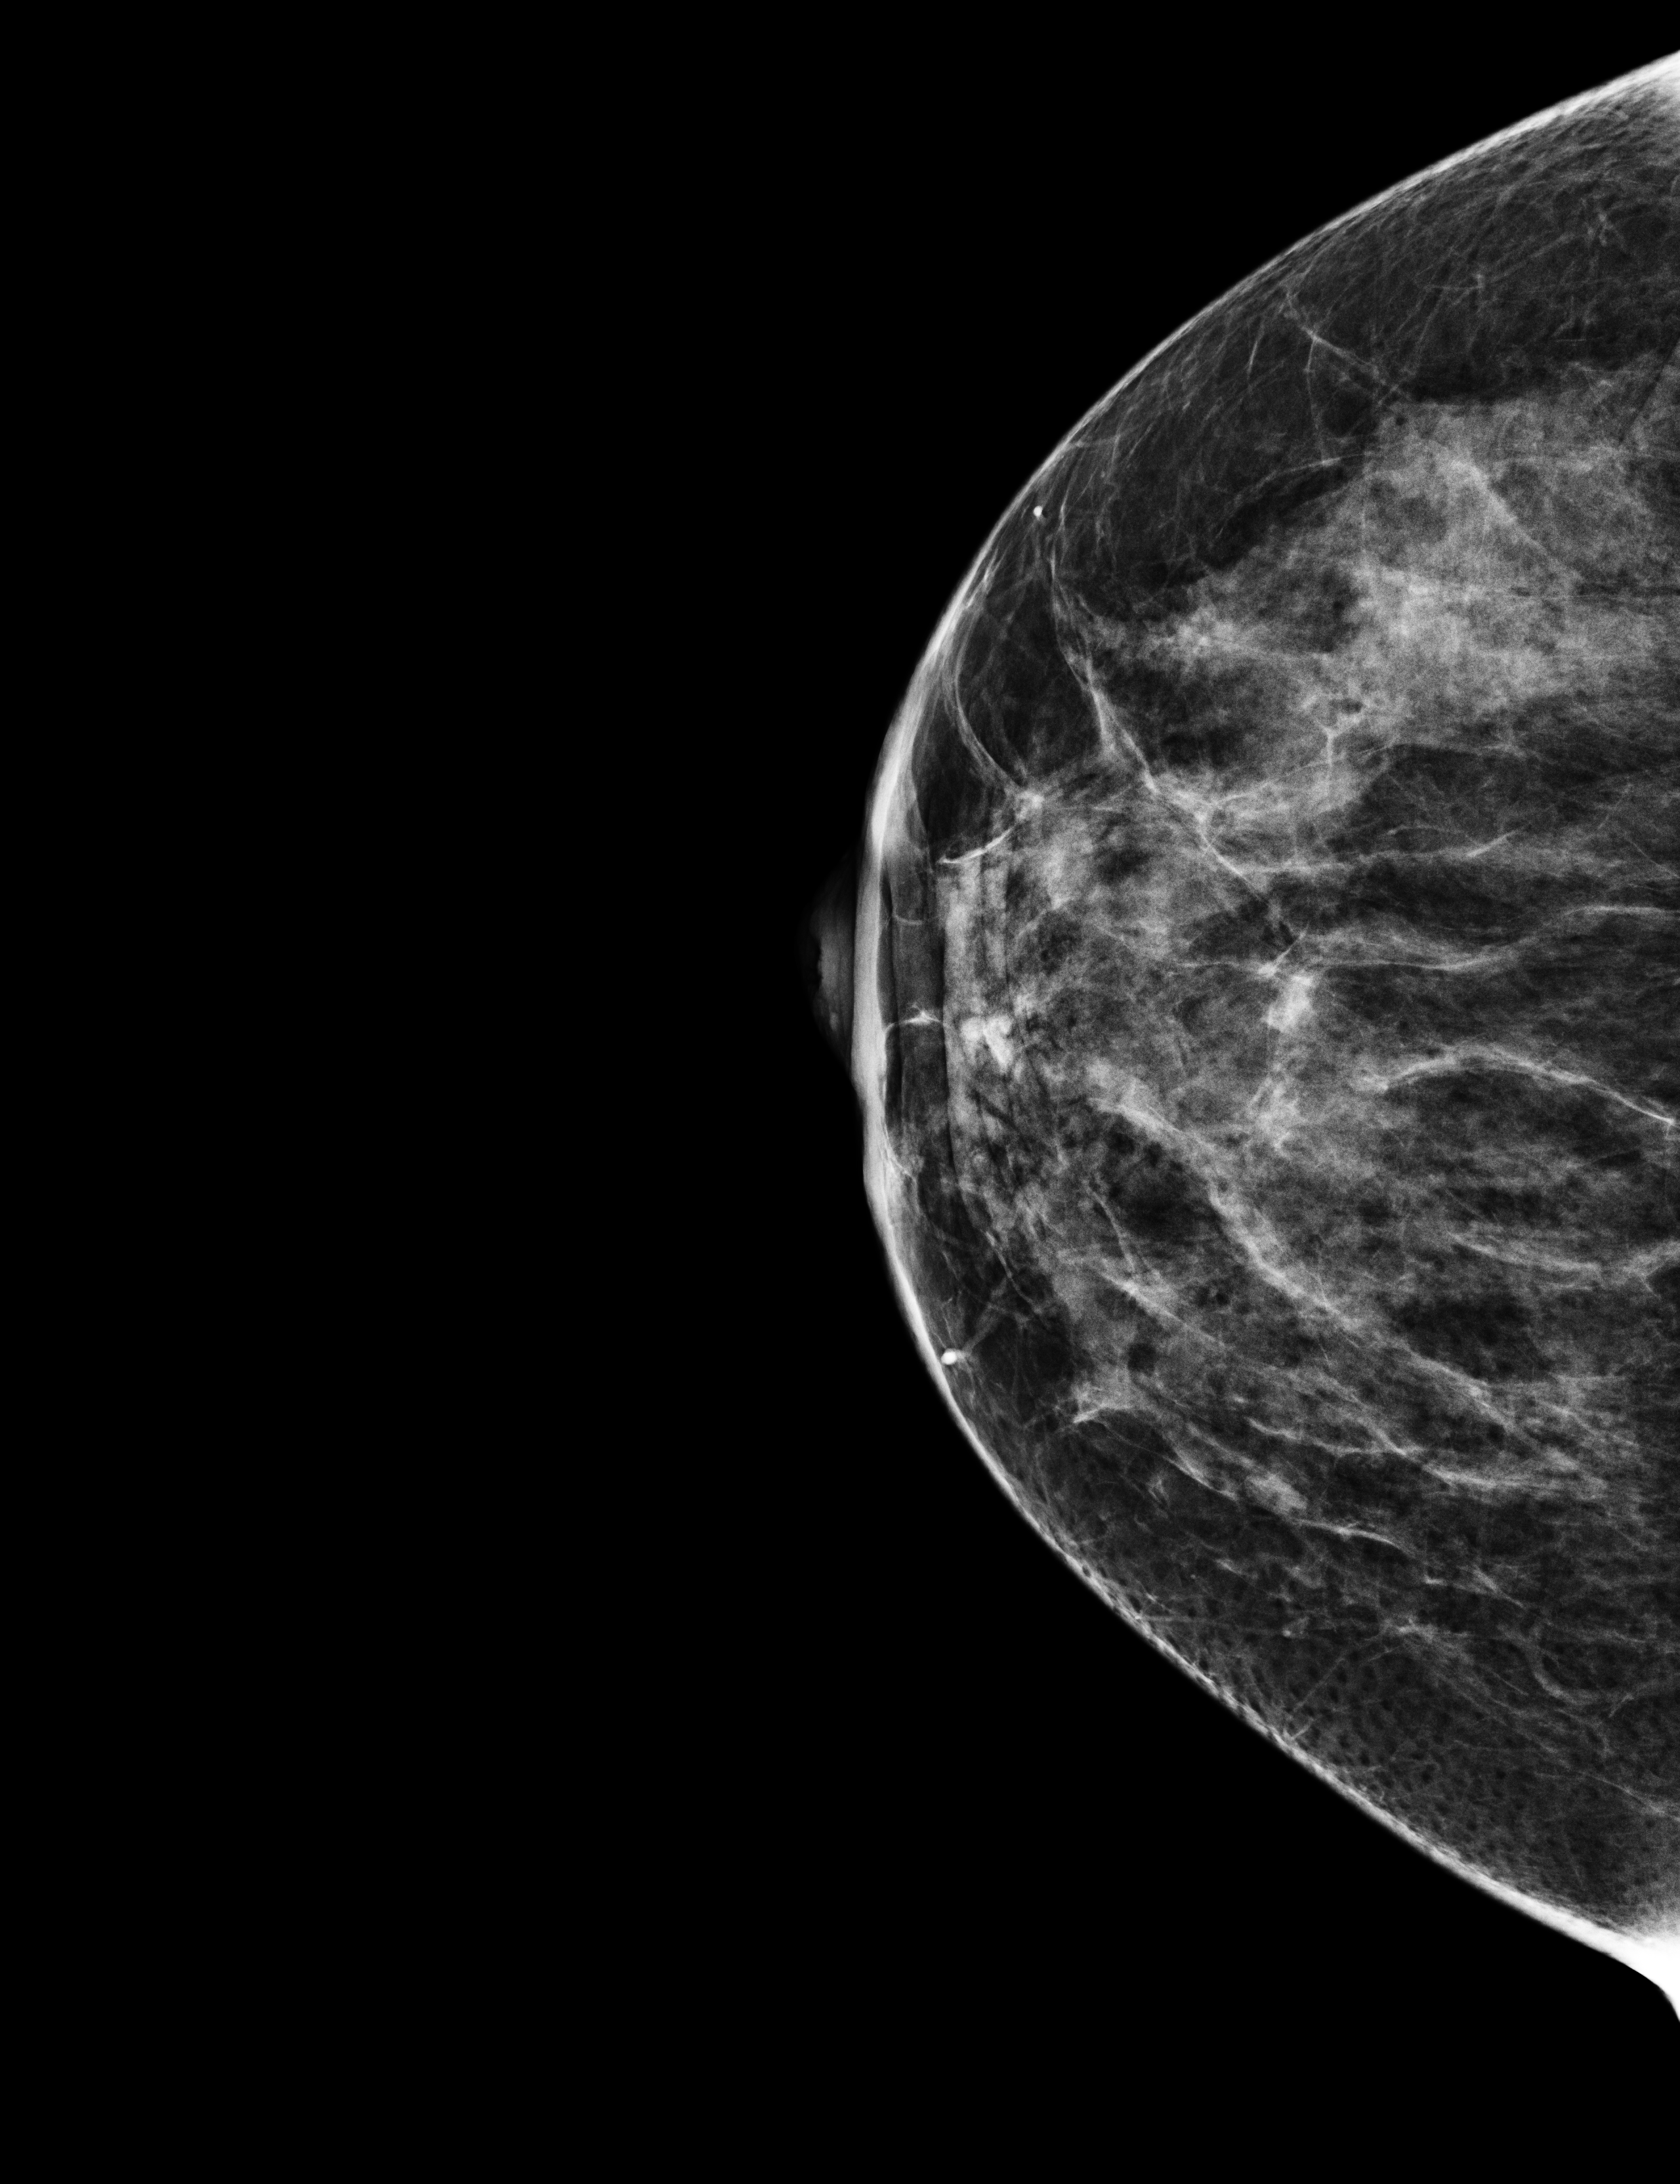
Digital mammogram (FFDM), right breast, craniocaudal (CC) view, screening examination. Female patient, age 42 years.
- BI-RADS breast density category at the screening exam (both breasts, scale 1–4): 3
- final BI-RADS category for the screening round (tomosynthesis exam, both breasts): category 1
- recall: no recall after this screen